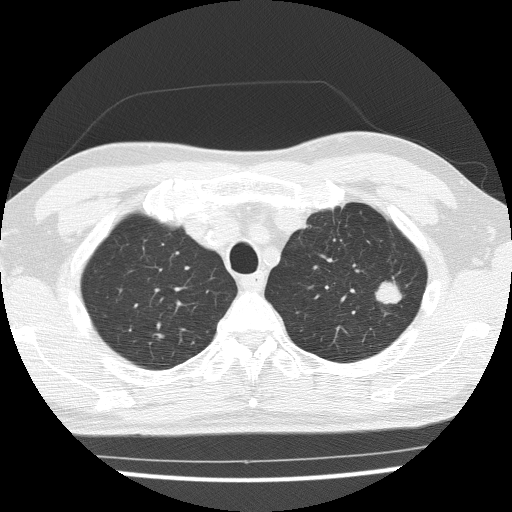
Axial slice from a low-dose chest CT screening exam; third annual screen; lung window (W 1500 / L -600 HU); 2 mm slice thickness; lung (sharp) reconstruction kernel (FC51); slice 33 of 154 in the series; 512 × 512 image matrix. Male, age 65 years at enrolment. Current smoker at enrolment.
Expert-annotated lung lesion, bounding box [x1, y1, x2, y2] px = [358, 273, 412, 320]. Reader record for this screening exam (exam-level; its link to the box is not recorded): non-calcified nodule or mass ≥4 mm, left upper lobe, 16 × 15 mm, poorly defined margins, soft tissue attenuation, pre-existing on the prior screen: yes; interval growth: yes. Participant outcome: lung cancer diagnosed 42 days after this screen — squamous cell carcinoma, NOS, left upper lobe, moderately differentiated (G2), stage IA (AJCC 6th edition), 25 mm at pathology.